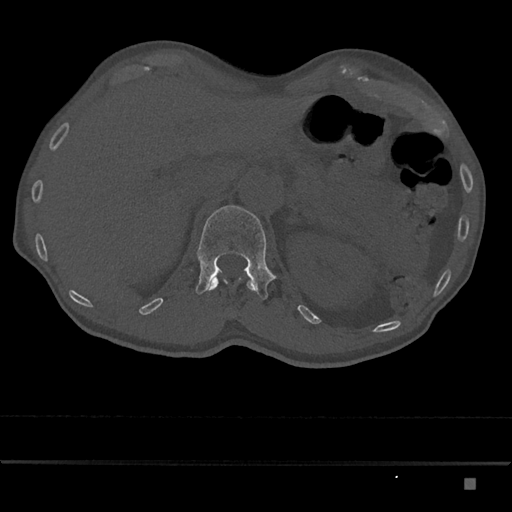
CT including the spine, one axial slice. Position 567 of 797 along the scan axis. Reconstruction kernel Br40s/3. 120 kVp. Bone window (W 1800 / L 400 HU). 0.5 mm slice thickness. 512 × 512 image matrix, field of view 390 × 390 mm. Patient: male, 72 years. Case-level facts recorded for this patient, not image findings: primary cancer: prostate.
Annotated regions visible in this slice (semi-automatically segmented with operator editing):
- L1 vertebra: bounding box <195,205,276,300> (left, top, right, bottom; pixels)
- T12 vertebra: <206,276,257,291>